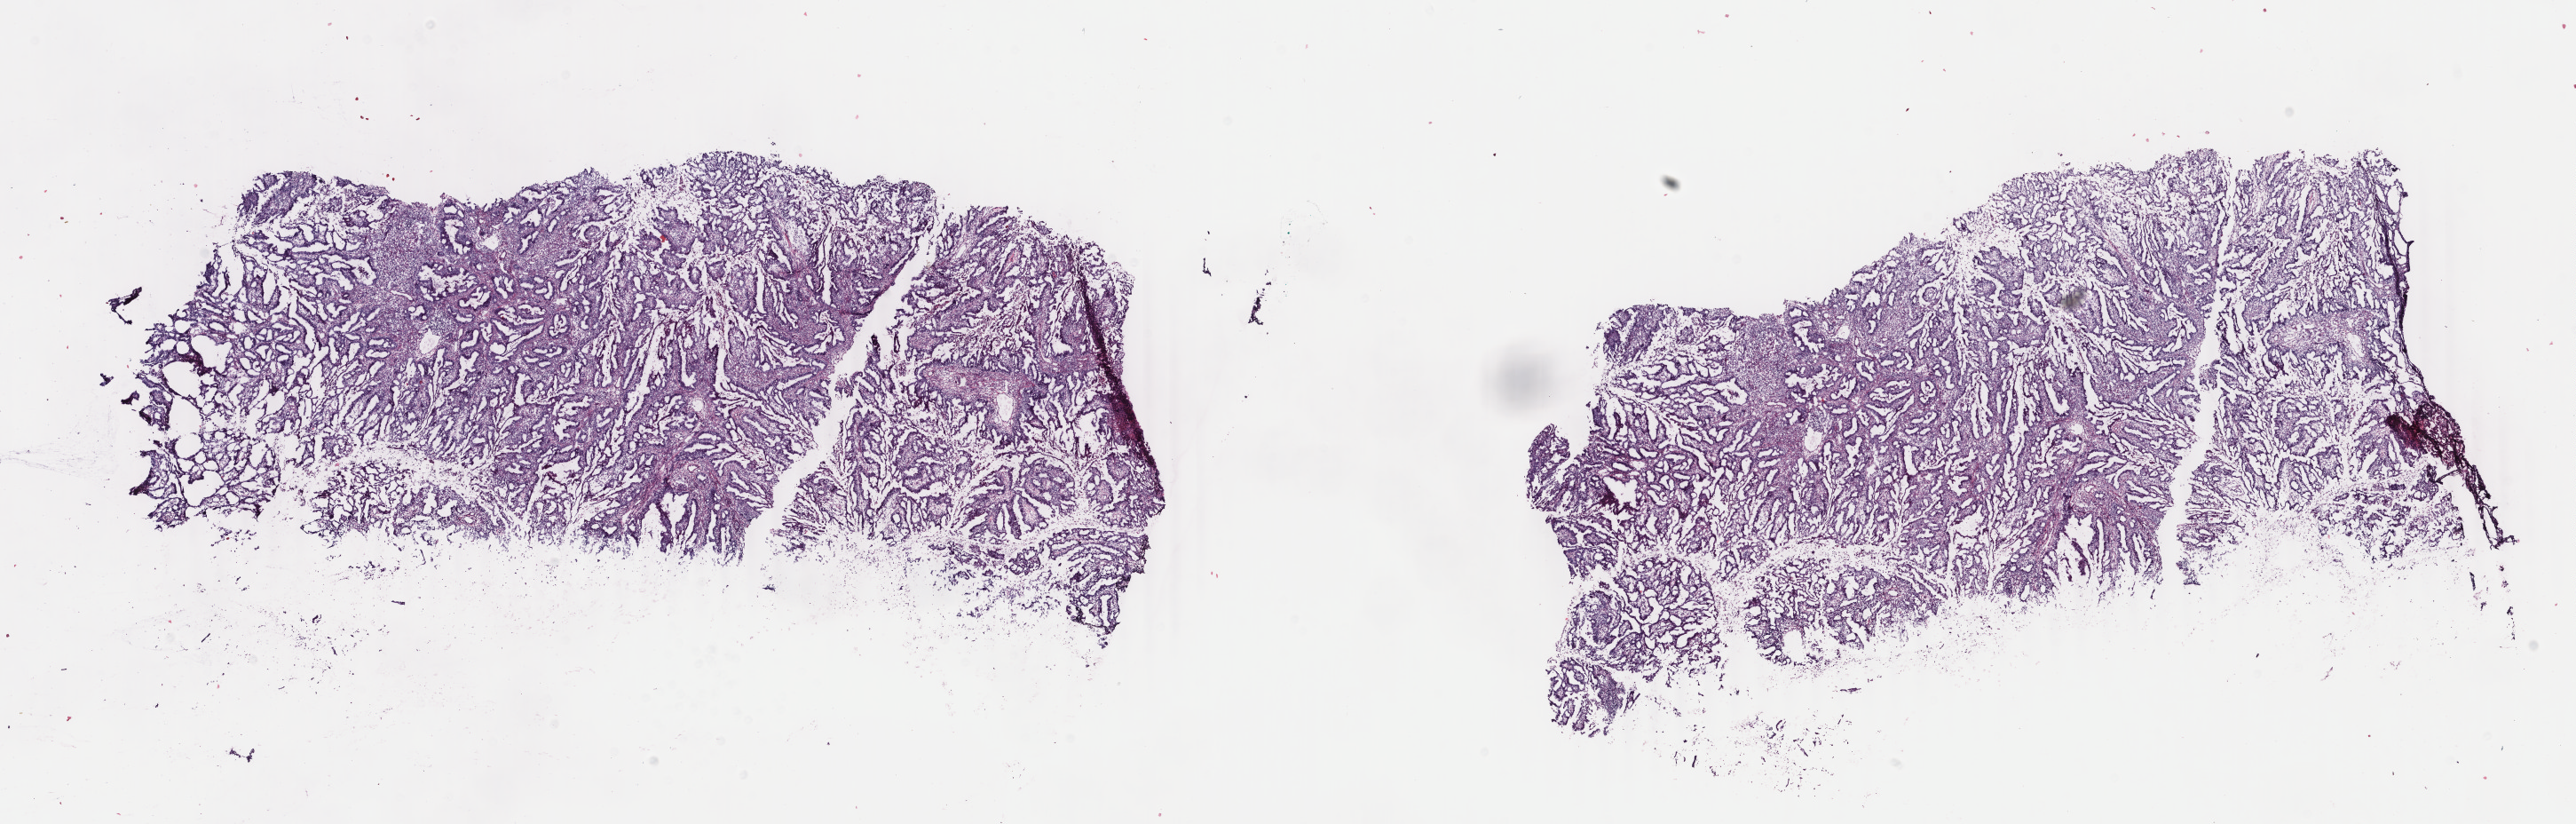
H&E-stained whole-slide image, a low-resolution overview of the entire scanned area, about 23.1 x 7.4 mm (from a 40x scan); frozen section; primary tumour sample from the uterus. Patient: female, age at initial diagnosis 61 years. Histologic grade: G2 (moderately differentiated). Slide review estimates, as recorded: tumour cells 20%, tumour nuclei 20%, normal cells 30%, stromal cells 50%, necrosis 20%. Infiltration values recorded for this section: lymphocyte infiltration 20%, monocyte infiltration 0%, neutrophil infiltration 20%.
FIGO stage: IC. Diagnosis: Endometrioid adenocarcinoma, NOS (endometrium).